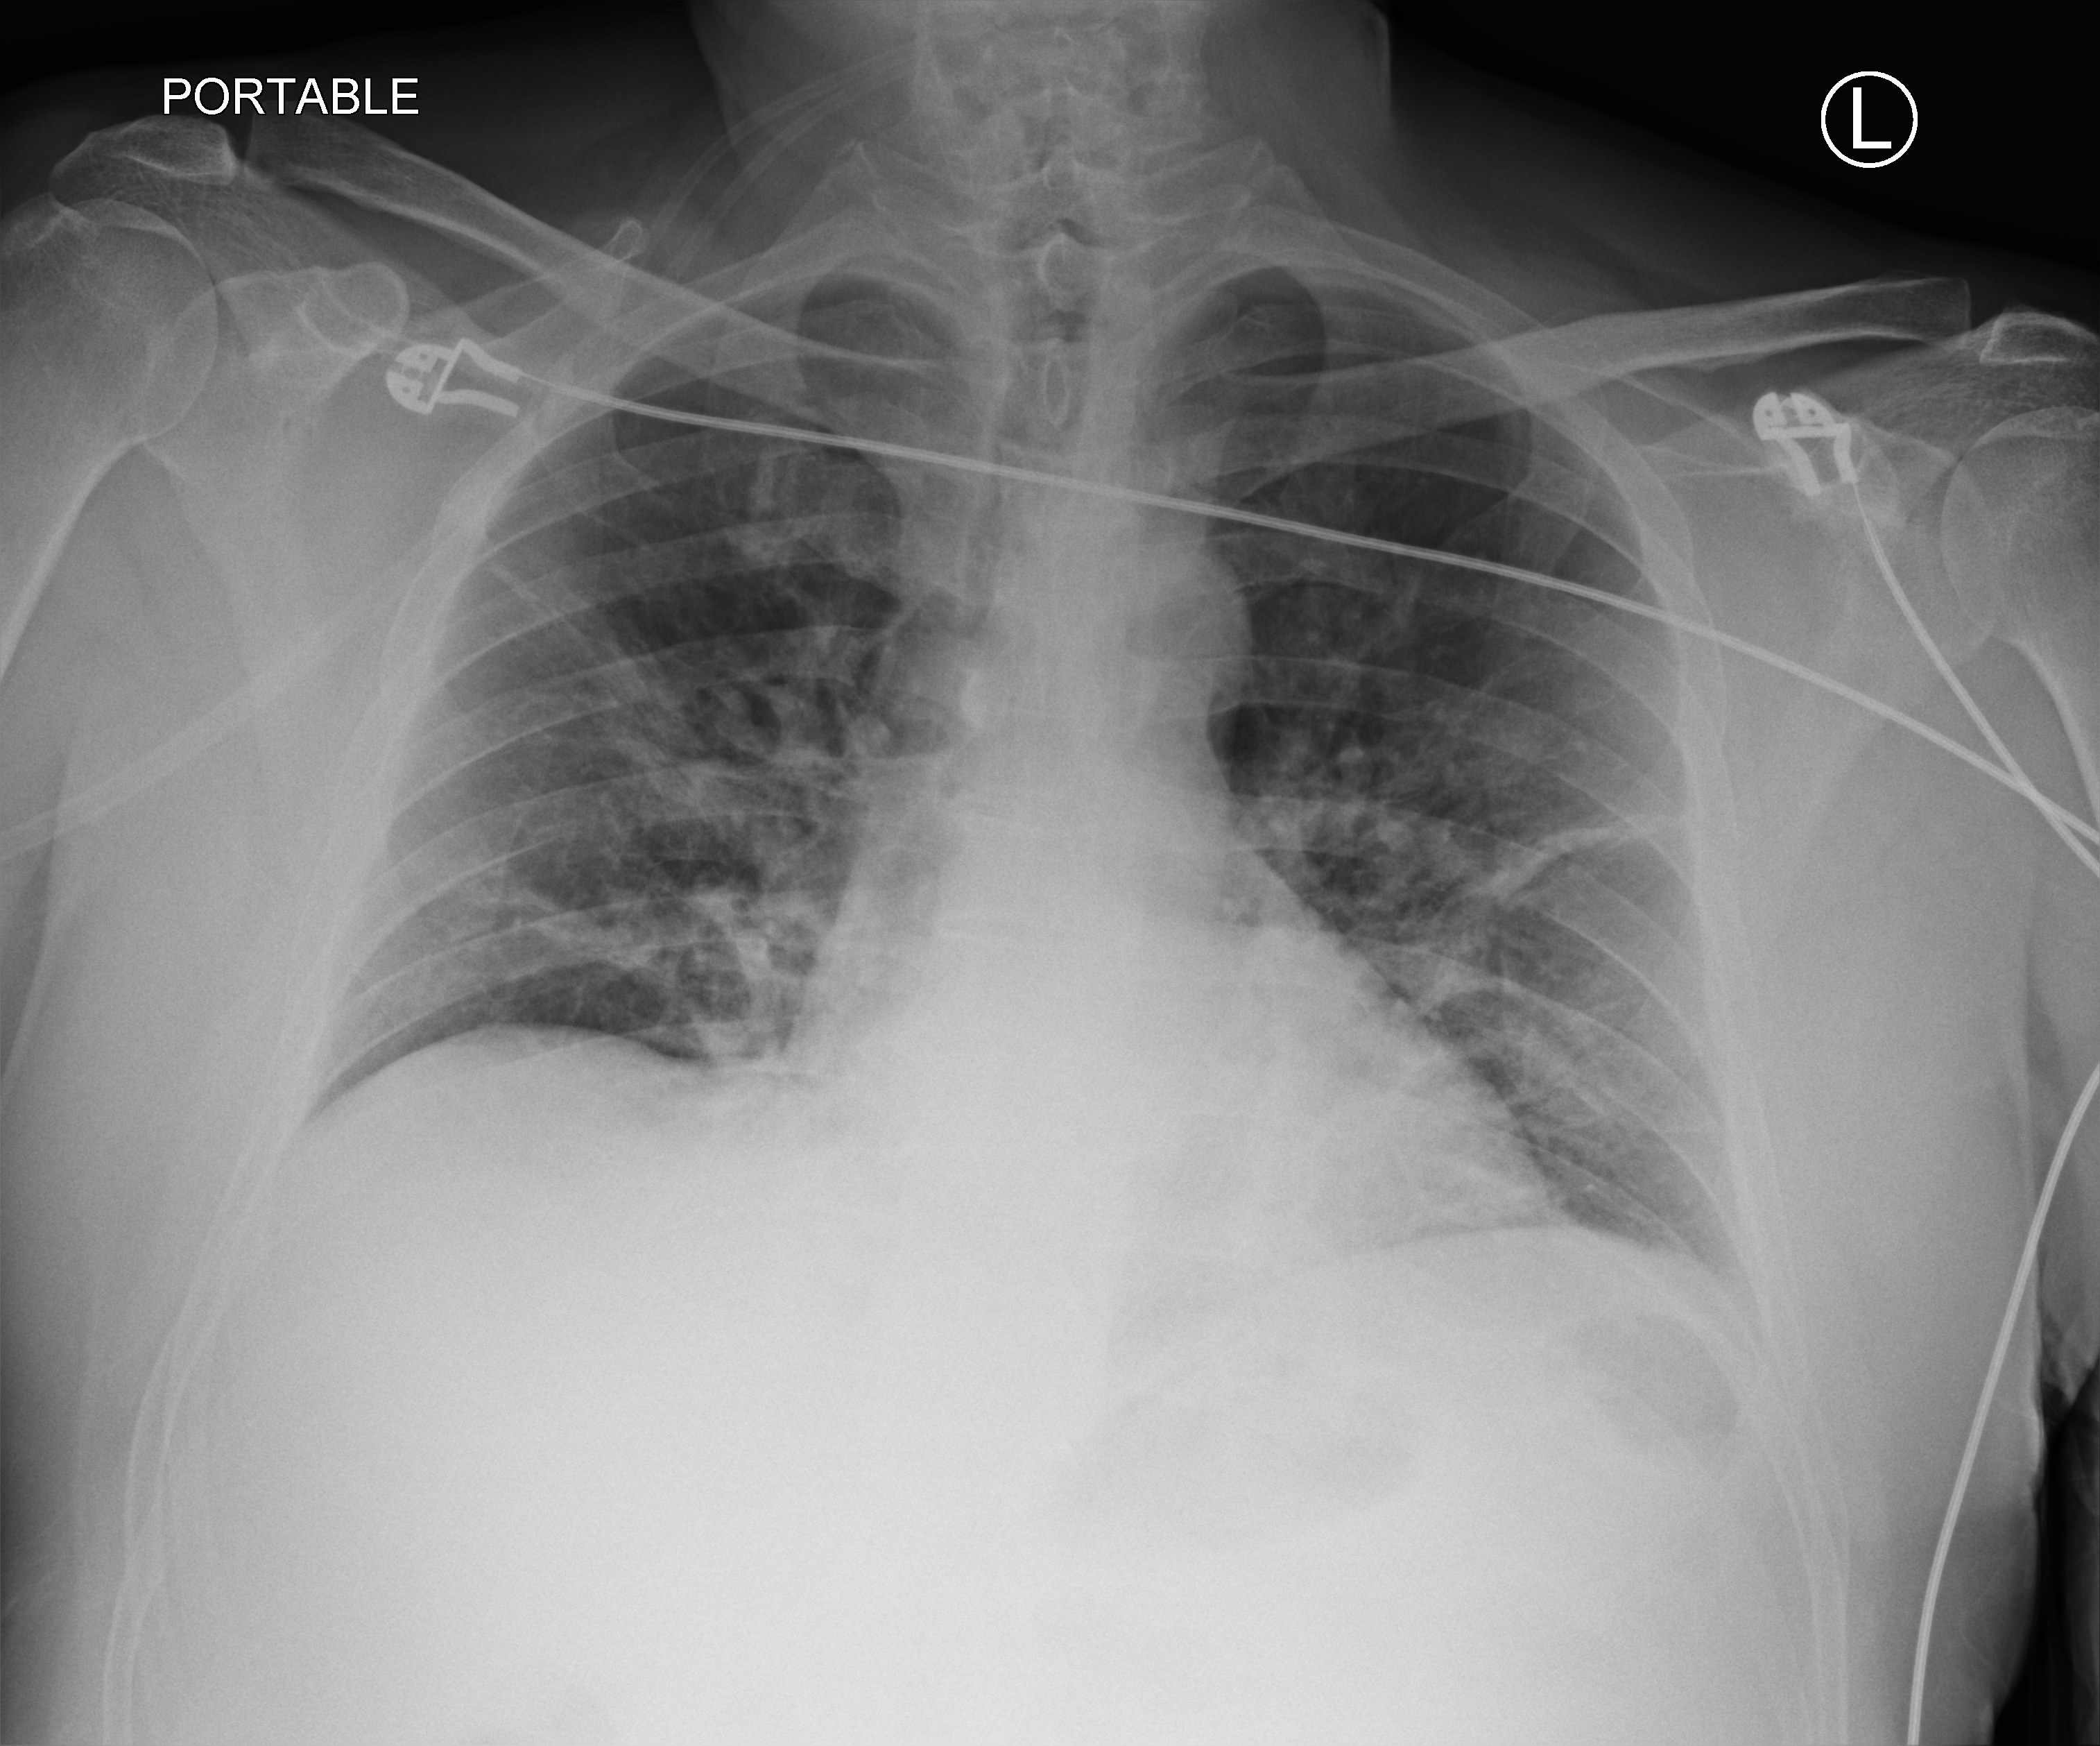
Portable chest radiograph, anteroposterior (AP) projection. Patient hospitalised with COVID-19; male, aged 18–59 years.
Admission-level facts for this patient (not findings on this image; timing relative to this image not recorded): length of hospital stay: 9 days; mechanically ventilated during this hospital stay: no.